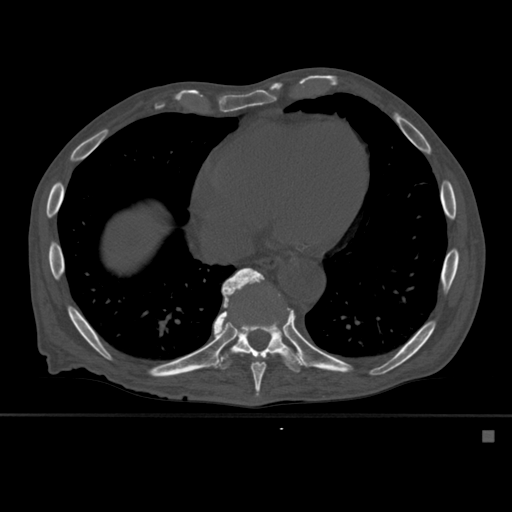
CT including the spine, one axial slice; slice 324 of 527 in the series (ordered by position); bone window (W 1800 / L 400 HU); 1.5 mm slice thickness; 512 × 512 image matrix. Patient: male, 78 years. Case-level facts recorded for this patient, not image findings: primary cancer: prostate.
Outlined on this slice (semi-automatically segmented with operator editing):
- T10 vertebra: bounding box [x1, y1, x2, y2] px = [217, 299, 304, 373]
- T9 vertebra: [222, 268, 296, 398]